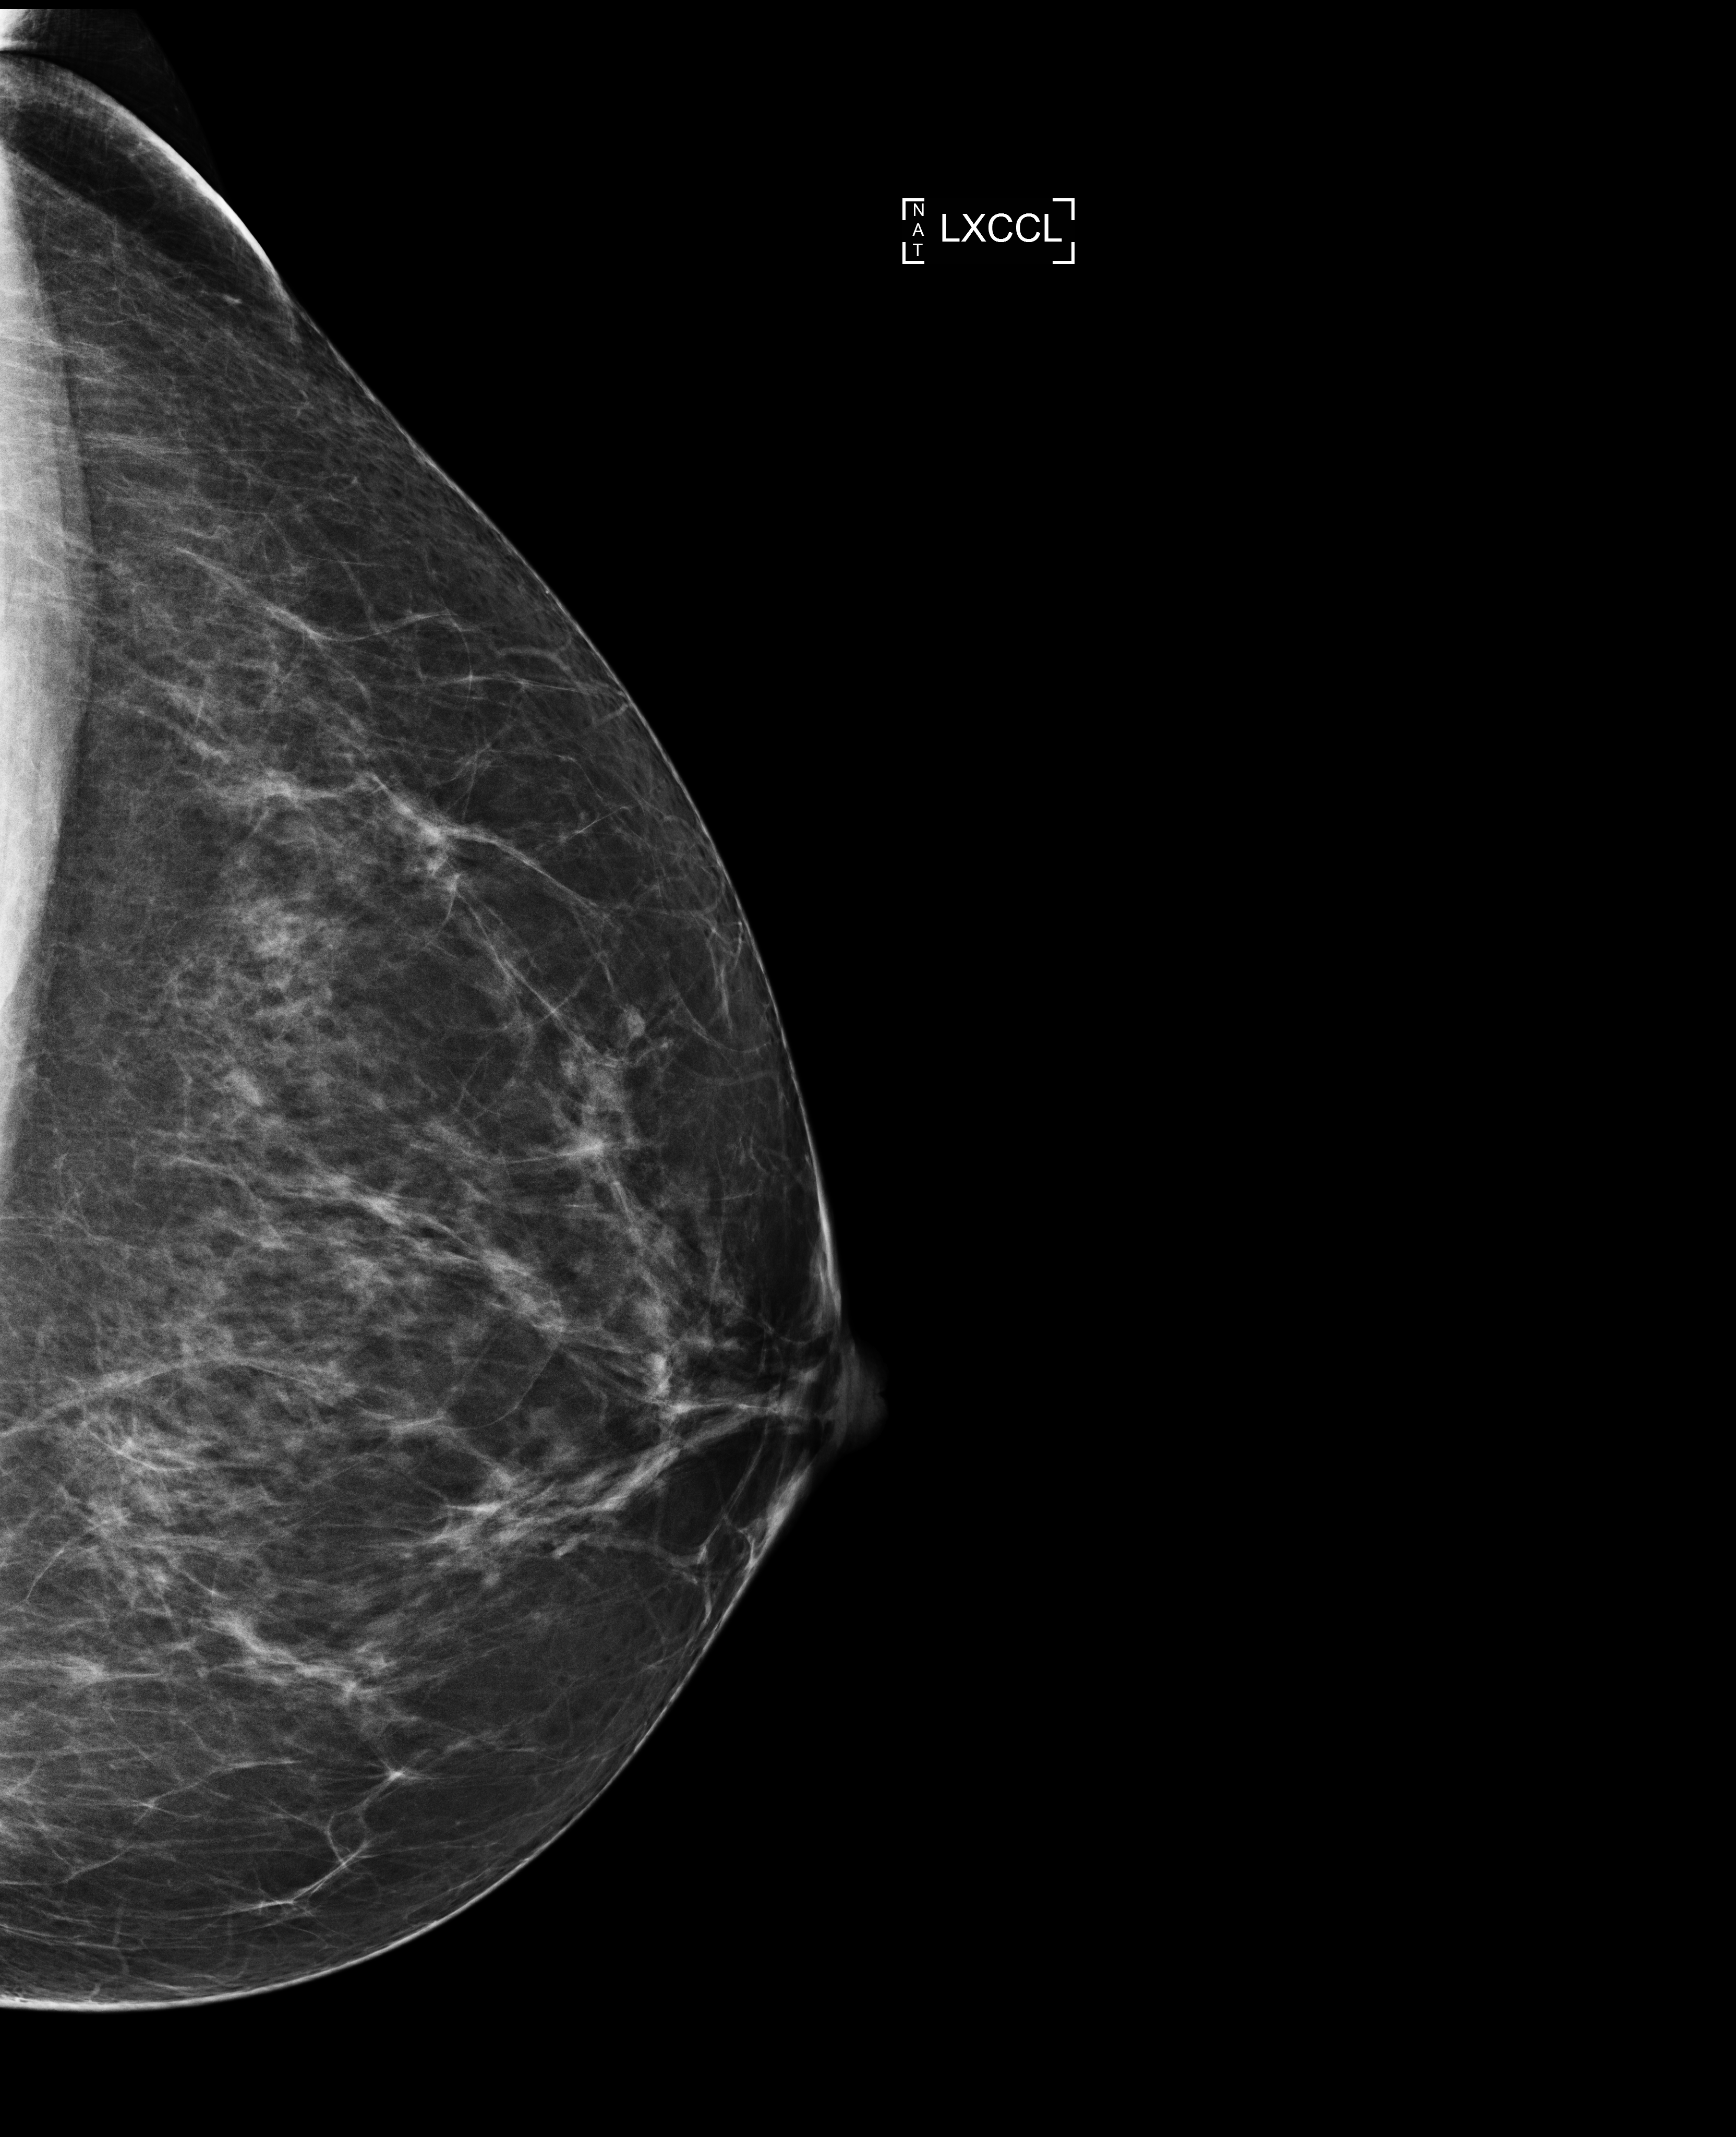
Digital mammogram (FFDM); left breast; laterally exaggerated craniocaudal (XCCL) view; screening examination; system: Selenia Dimensions. Female patient, age 52 years.
BI-RADS breast density category at the screening exam (both breasts, scale 1–4): 2. Final BI-RADS category for the screening round (tomosynthesis exam, both breasts): category 1. Recall: no recall after this screen.